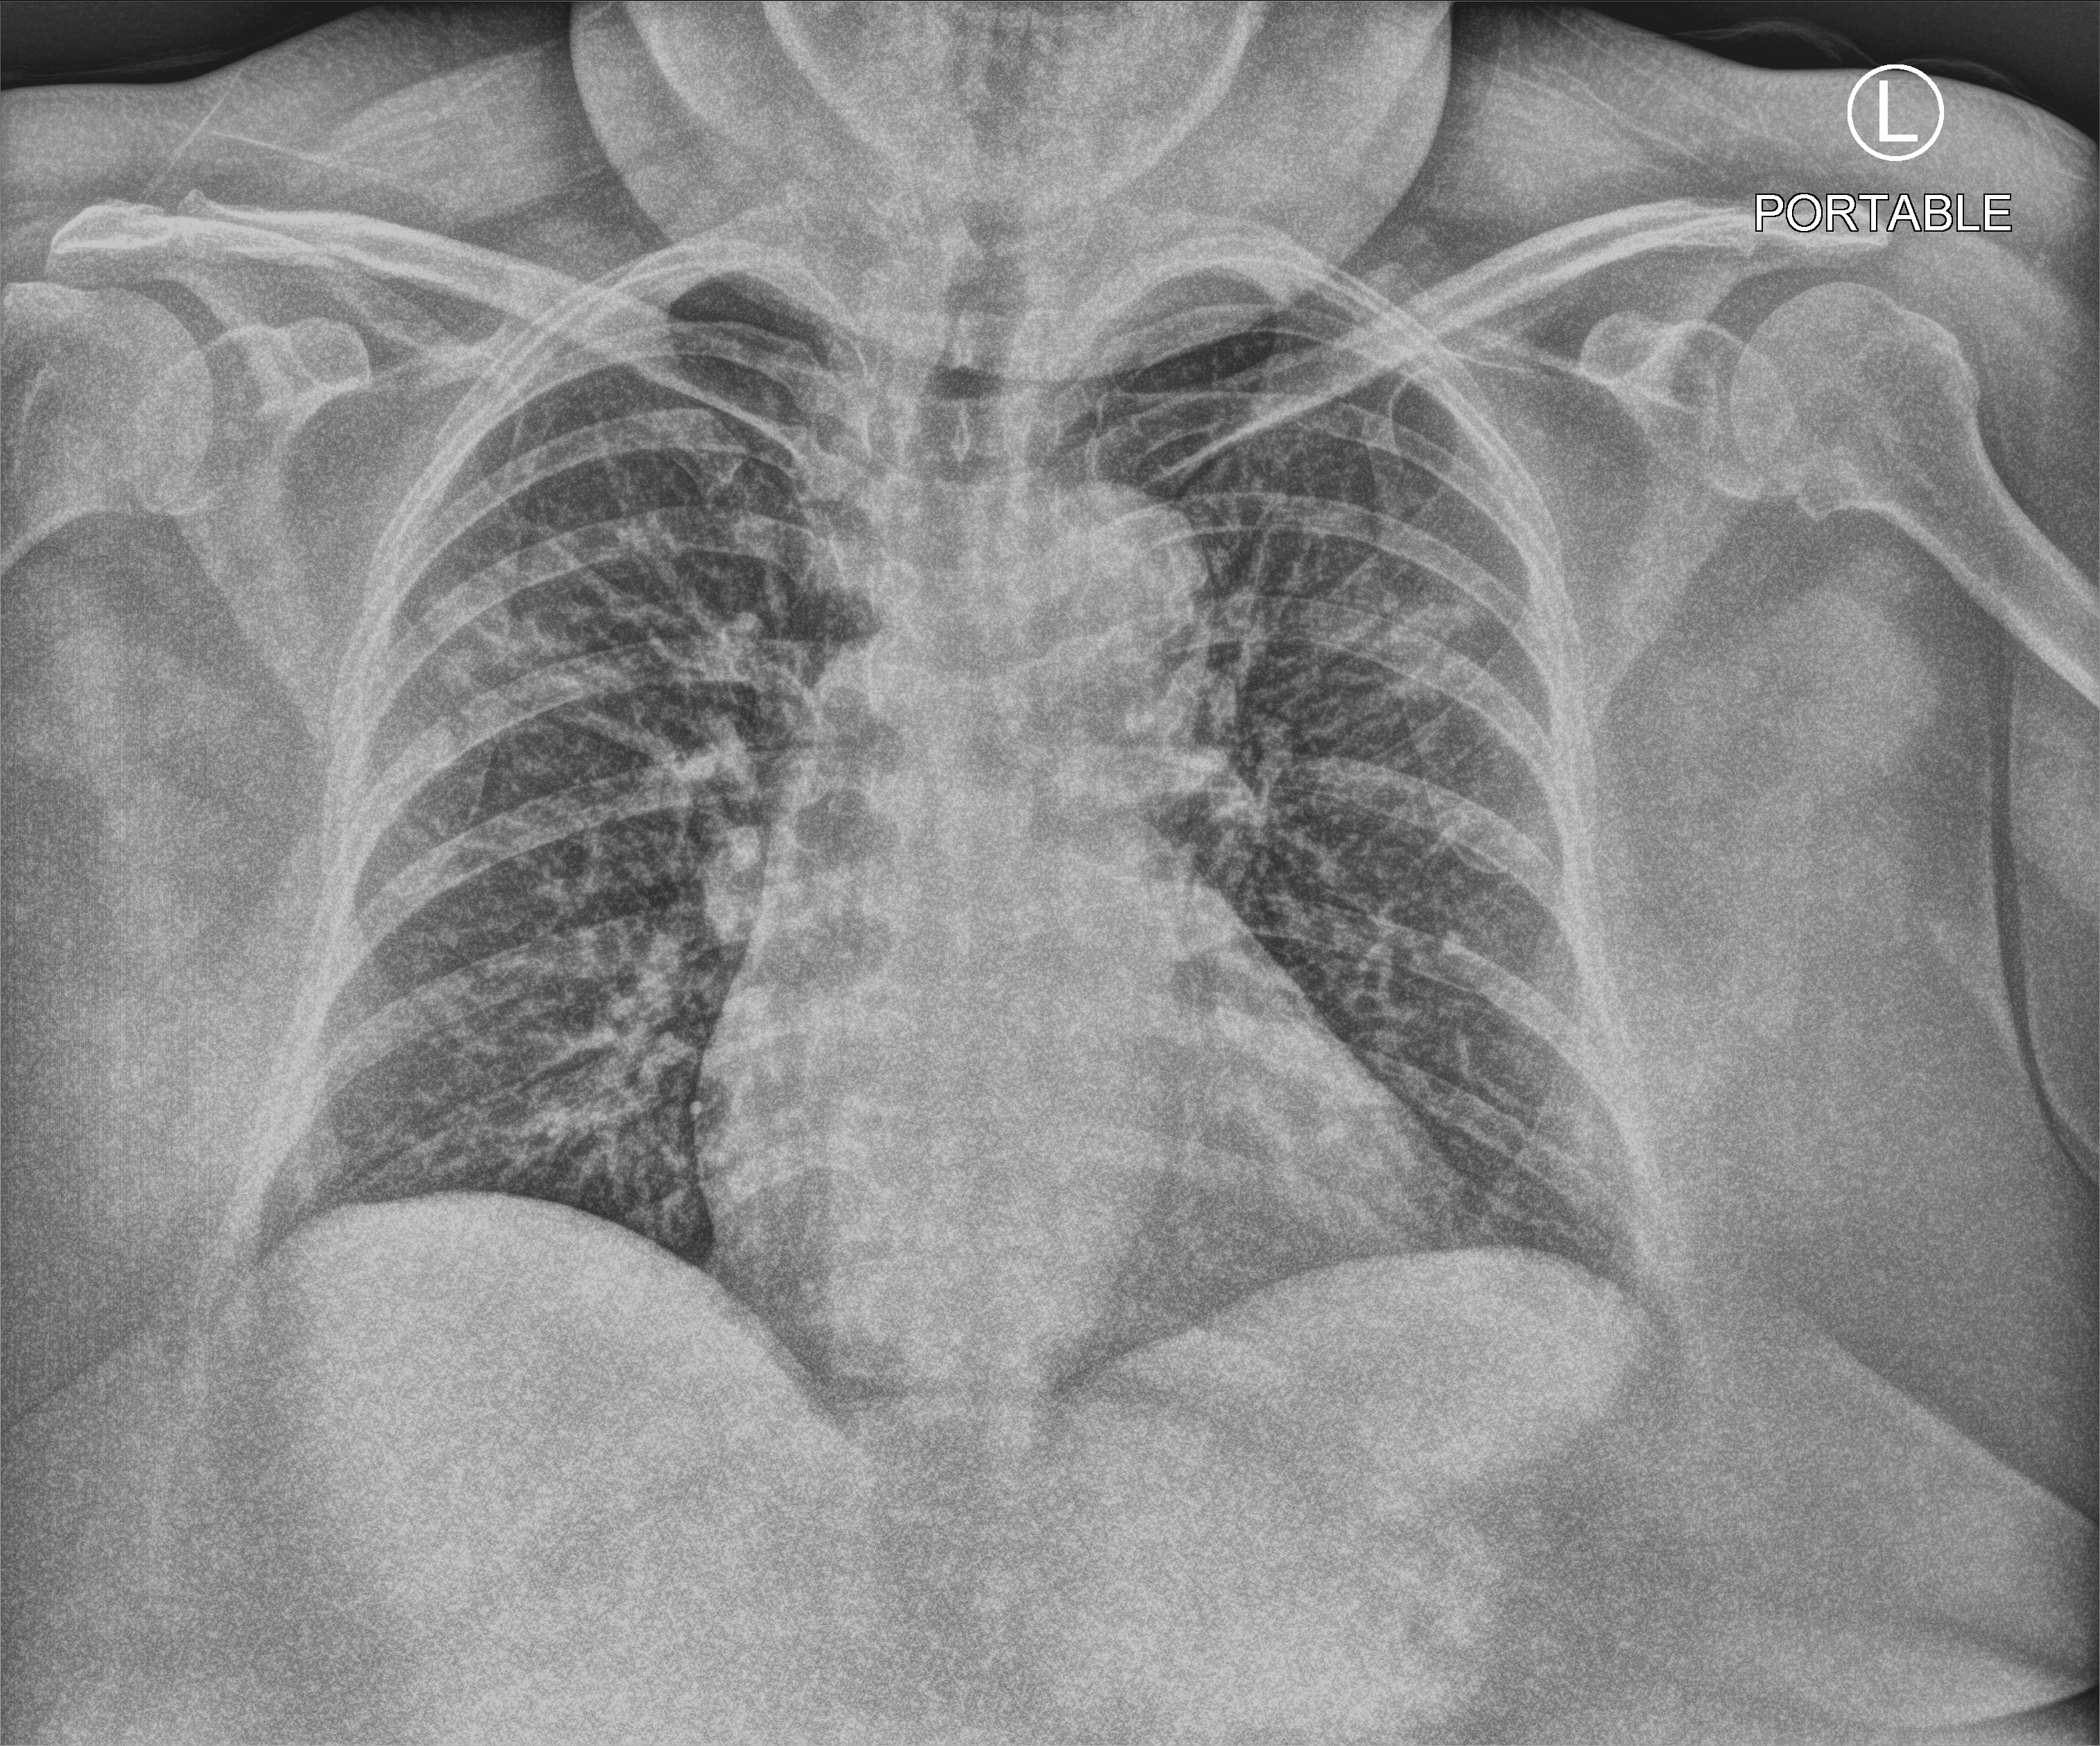
Chest X-ray (portable), anteroposterior (AP) projection. Female patient hospitalised with COVID-19, age 18–59 years.
From the hospital-stay record, not from the radiograph (when in the stay this image was taken is not recorded): hypertension (admission record): yes; admitted to intensive care during this hospital stay: no; length of hospital stay: 3 days.